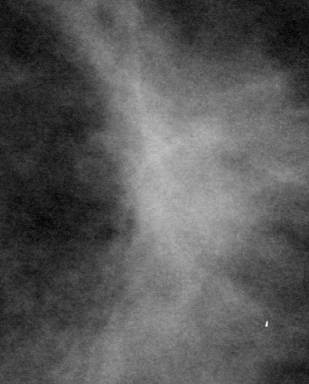
Cropped region of a digitized screen-film mammogram centred on a radiologist-marked abnormality, left breast, CC view.
Marked abnormality: mass, shape irregular / architectural distortion, margins spiculated; BI-RADS assessment category 4; subtlety rating 4 on a 1 (subtle) to 5 (obvious) scale; pathology (as recorded): malignant.